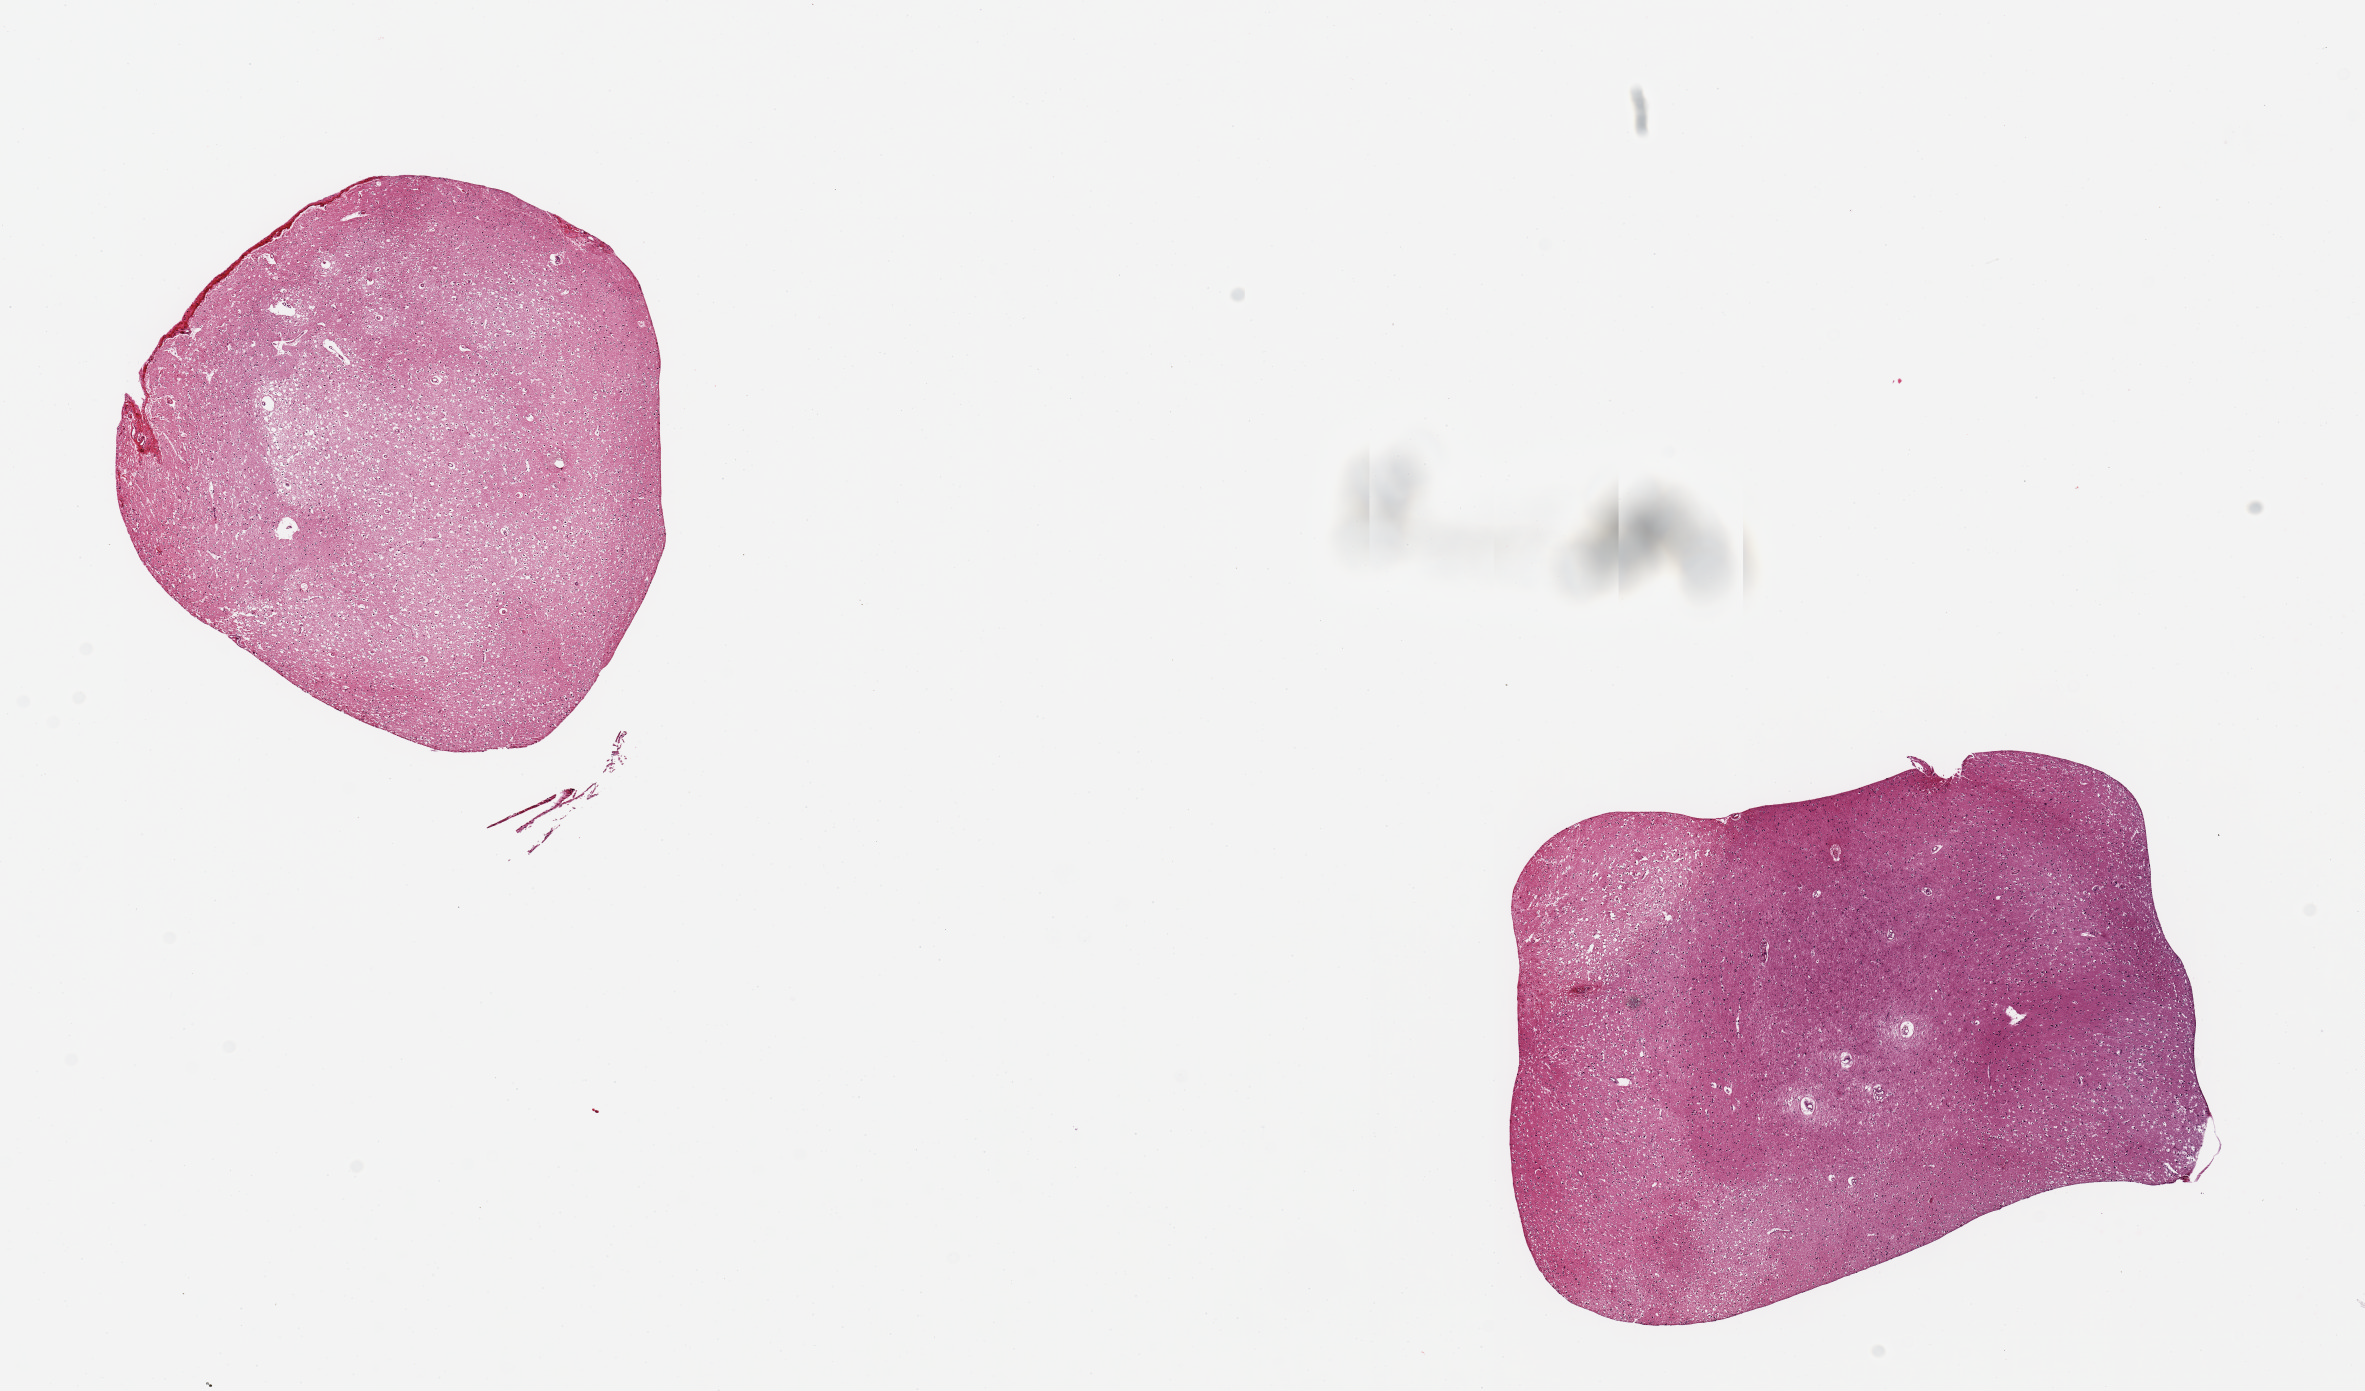
H&E whole-slide image, brightfield, a low-resolution overview of the entire scanned area, about 18.7 x 11.0 mm; PAXgene-fixed, paraffin-embedded tissue; target tissue: cerebral cortex; donor tissue sample. Donor sex: male.
• reviewer comment on this tissue sample: 2 pieces, 4x4 & 5.5x4mm